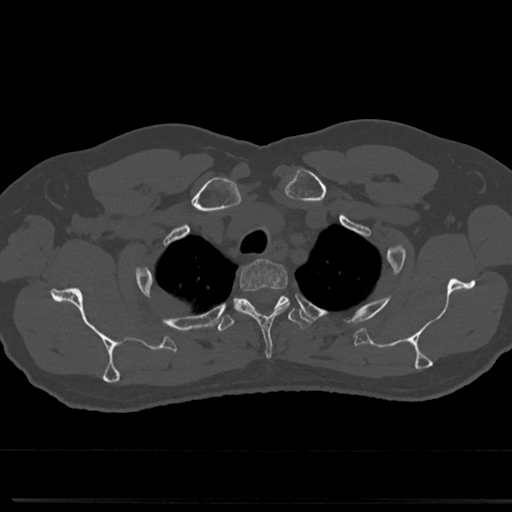
CT including the spine, one axial slice. Slice 616 of 817 in the series (ordered by position). 120 kVp. Bone window (W 1800 / L 400 HU). 0.5 mm slice thickness. 512 × 512 image matrix, field of view 355 × 355 mm. Male patient, age 61 years. From the clinical record (not read from this slice): primary cancer: prostate.
Annotated regions visible in this slice (semi-automatic segmentation, software-assisted and operator-edited):
- T2 vertebra: bounding box [x1, y1, x2, y2] px = [237, 261, 288, 317]
- T3 vertebra: [214, 293, 313, 334]